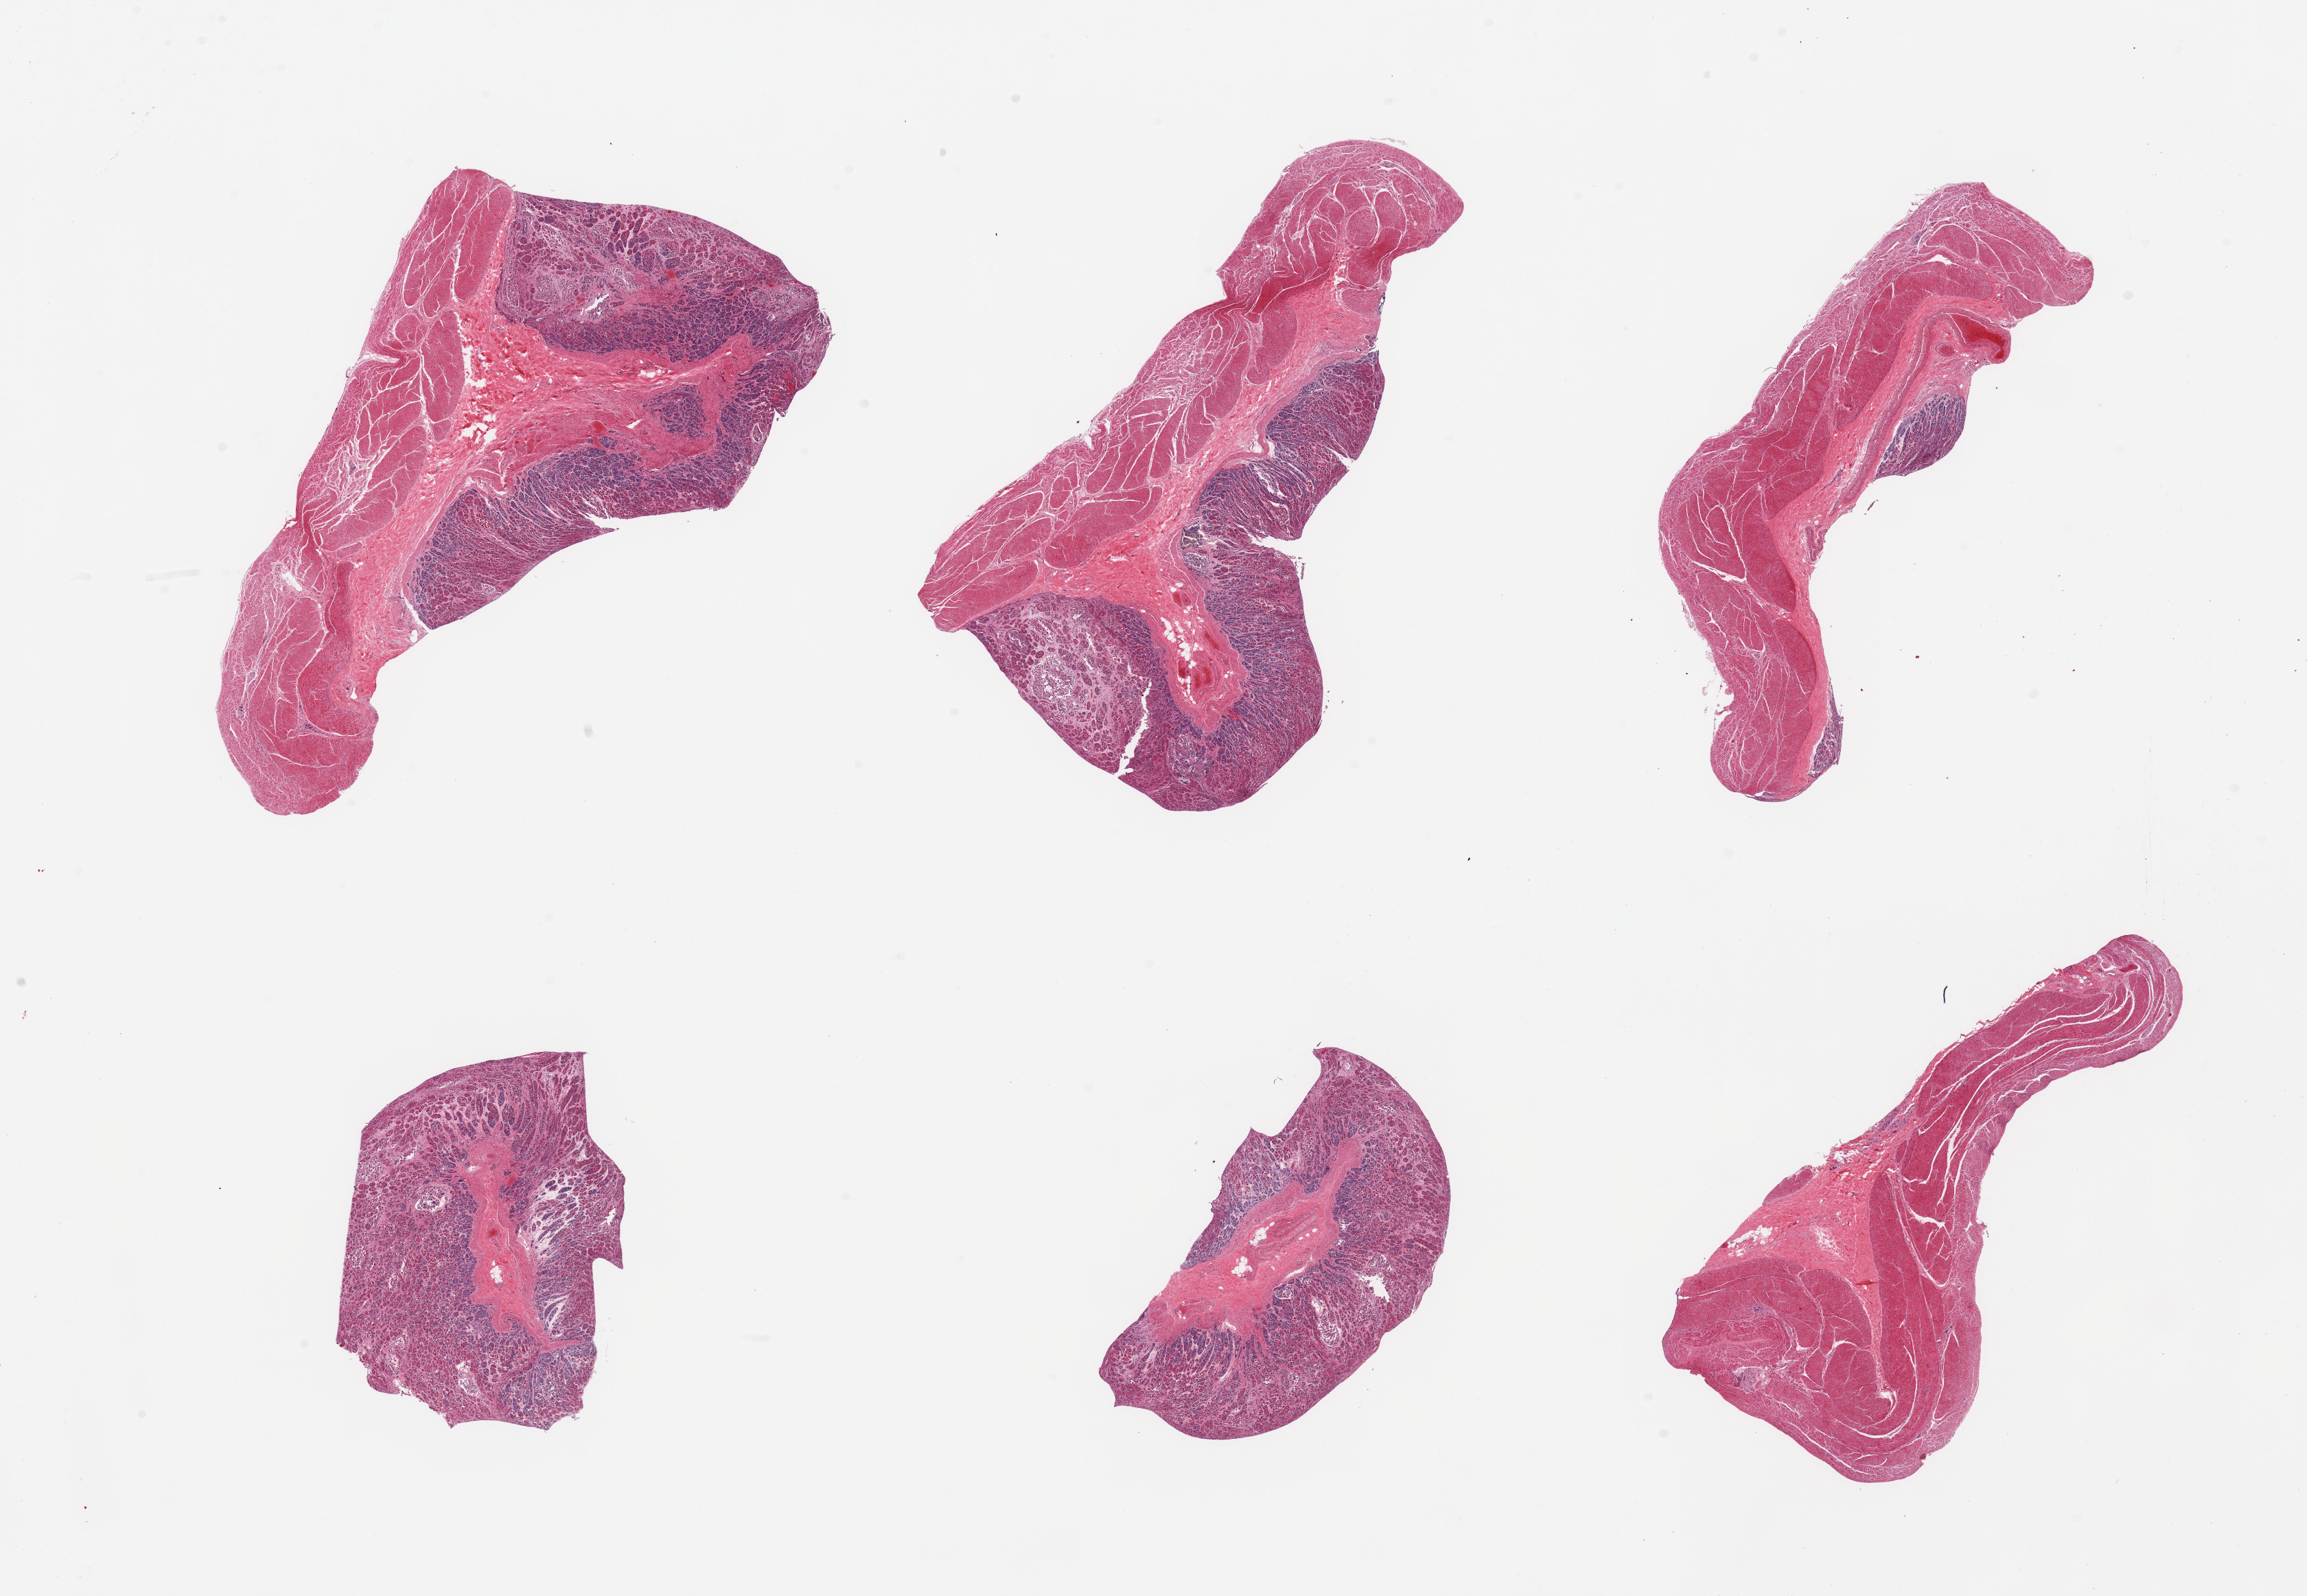
Digitized haematoxylin and eosin-stained section, brightfield, low-resolution overview of the scanned area, about 26.6 x 18.4 mm. PAXgene-fixed paraffin-embedded (PFPE) section. Section of stomach (target tissue). Donor tissue sample. Donor: male.
Reviewer comment on this tissue sample: 6 pieces: mucosa =2; muscle = 1; 3 with ample mucosa & muscle, 2 mucosa only, 1 muscle only.